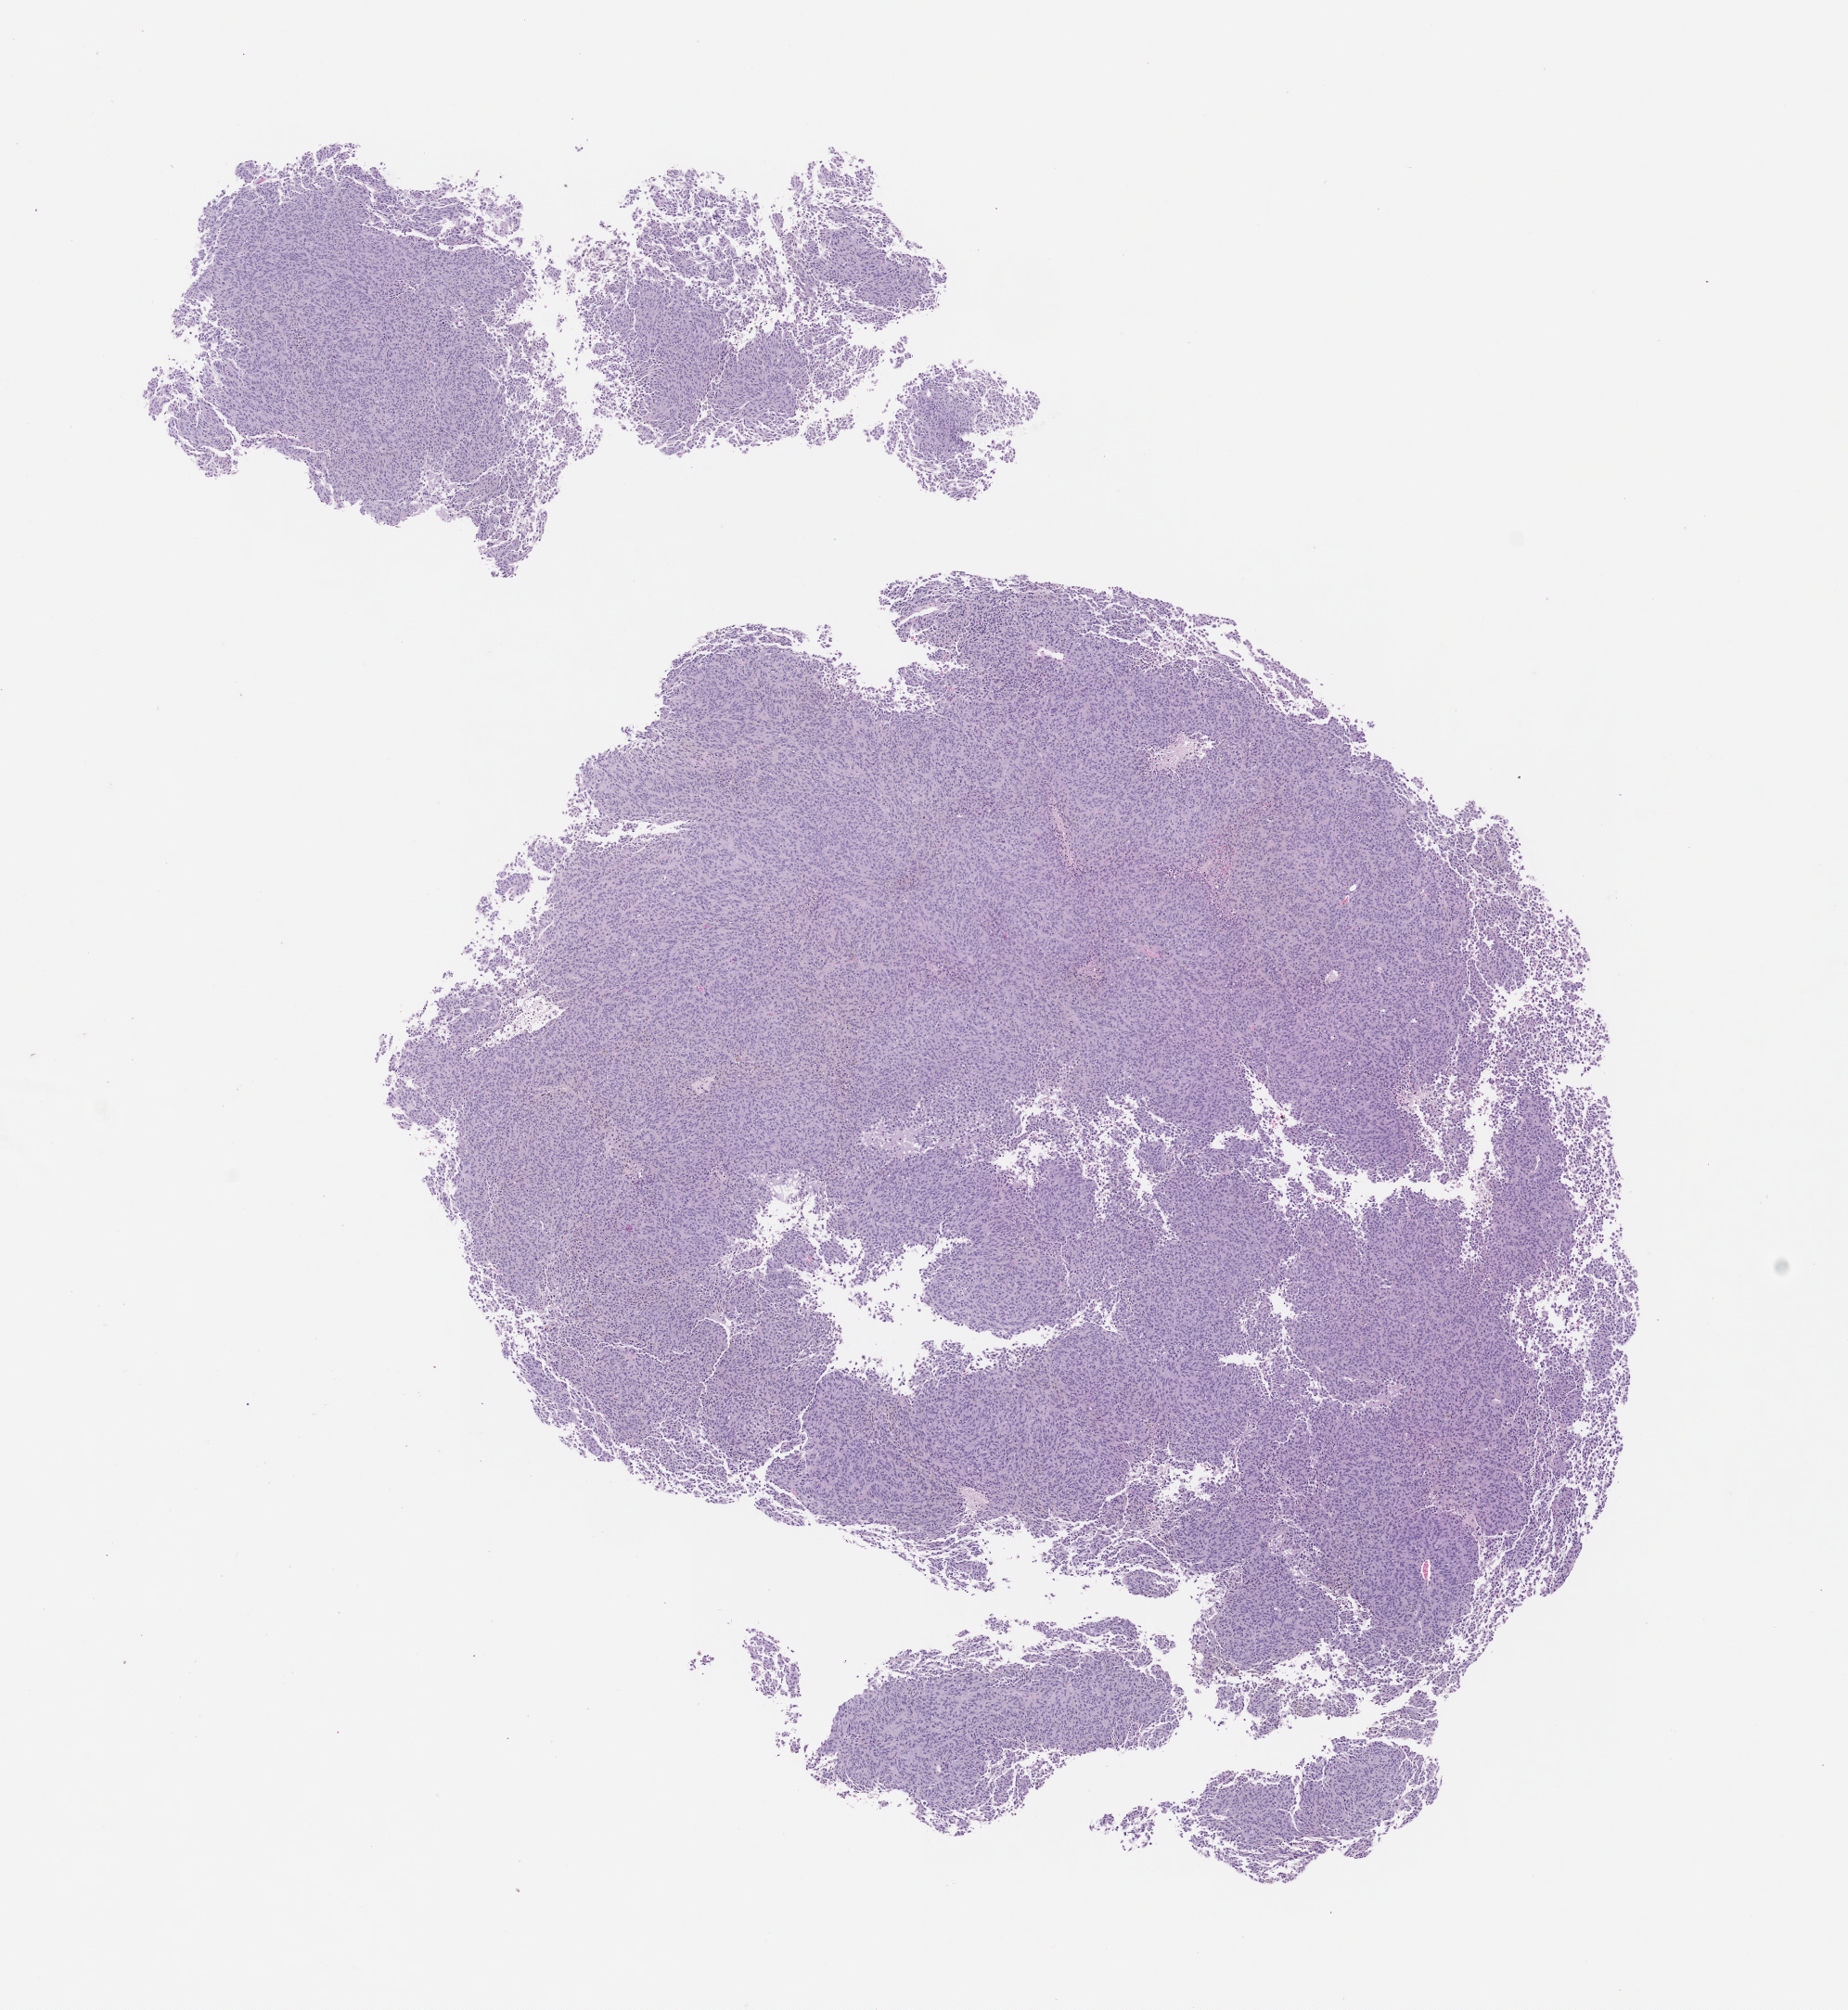
Whole-slide image, hematoxylin and eosin (H&E): patient-derived xenograft (human tumor grown in a mouse), passage 1, low-resolution overview of the scanned area, about 8.0 x 8.7 mm, formalin-fixed paraffin-embedded section, tumor site category: skin.
Originating patient diagnosis: Melanoma.